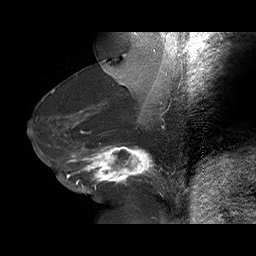
Breast MRI (dynamic contrast-enhanced), one sagittal slice; slice 35 of 75 in the series (ordered by position); dynamic contrast-enhanced series, time point 2 of 6 at this slice position (early post-contrast); 1.5 T; TE 4.5 ms, TR 32.4 ms; 3 mm slice thickness; 256 × 256 image matrix. Female patient. Case-level facts recorded for this patient, not image findings: setting: breast cancer imaged before/during neoadjuvant chemotherapy; receptor status: HR-positive, HER2-negative.
Outlined on this slice (semi-automatically segmented with operator editing):
- analysis volume of interest (the breast-tissue region the enhancement analysis was run in; not a lesion): box from (x=58, y=134) to (x=166, y=191) px
- tumour enhancement mask (voxels above the 100 % enhancement threshold inside the analysis volume of interest): (x=66, y=146)–(x=157, y=184)